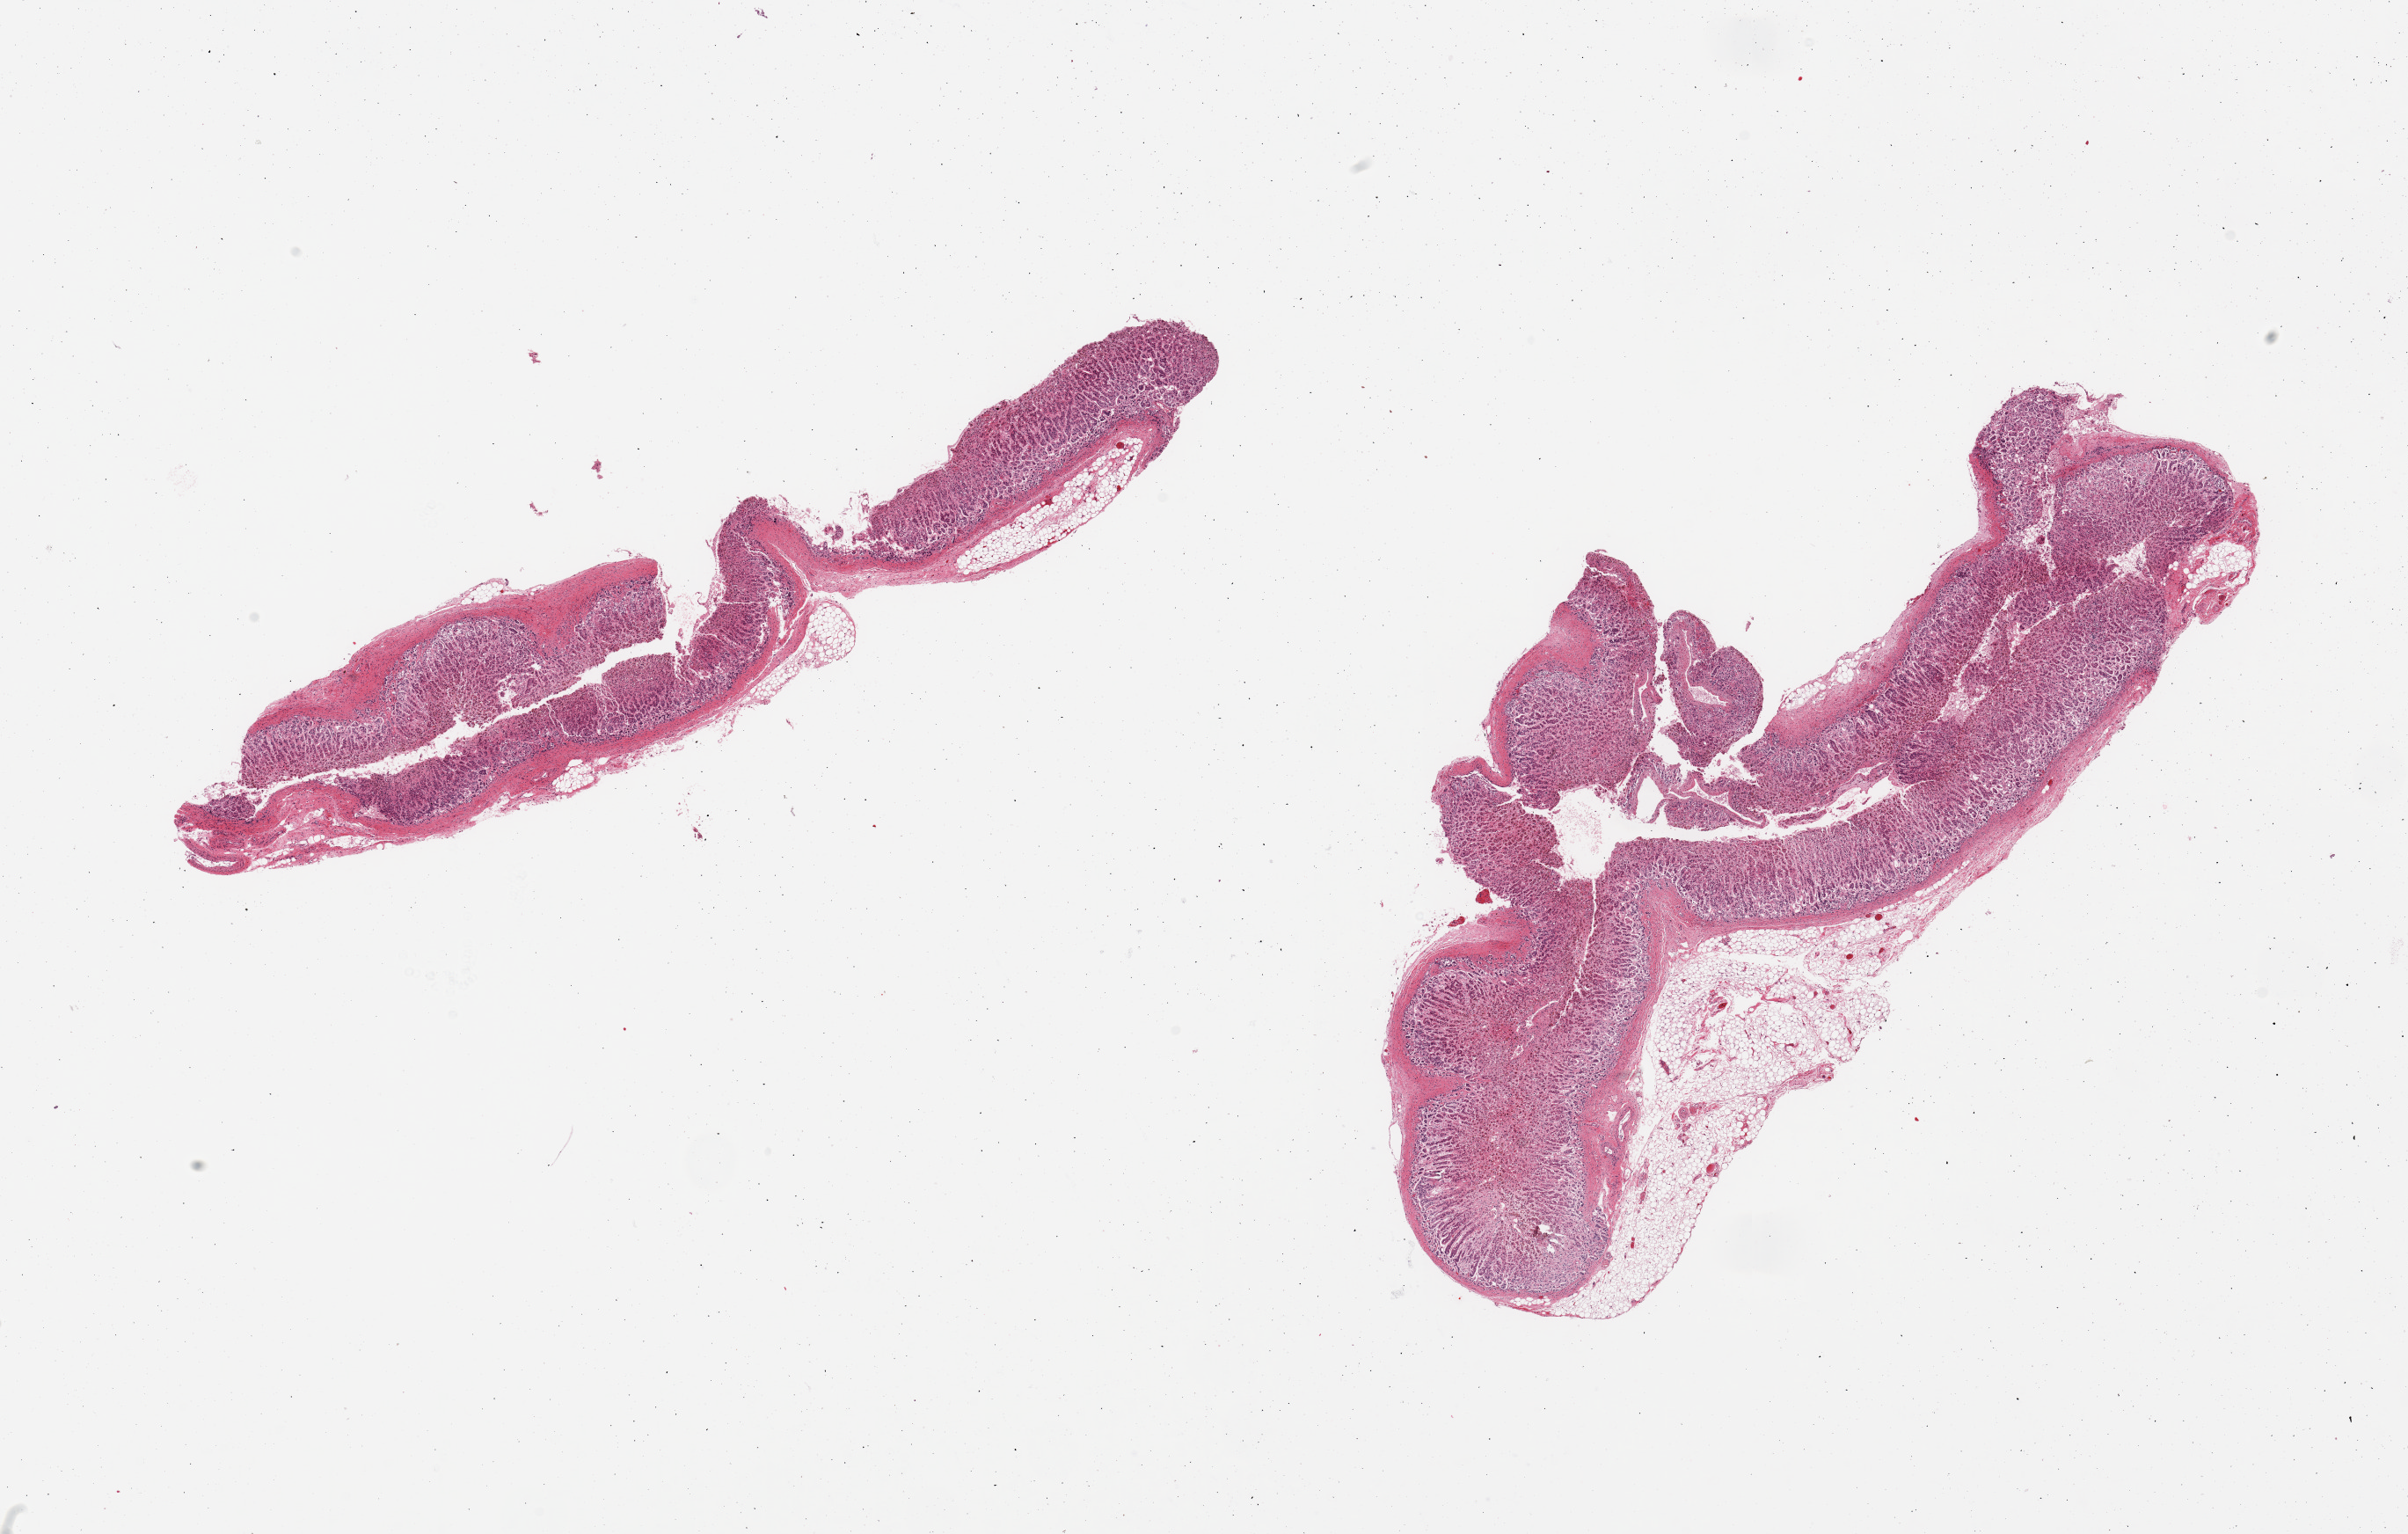
Digitized hematoxylin and eosin (H&E)-stained section, brightfield — low-resolution overview of the scanned area, about 21.7 x 13.8 mm; PAXgene-fixed, paraffin-embedded tissue; section of adrenal gland (target tissue); donor tissue sample.
Reviewer comment on this tissue sample: 2 pieces; 30% external fat.